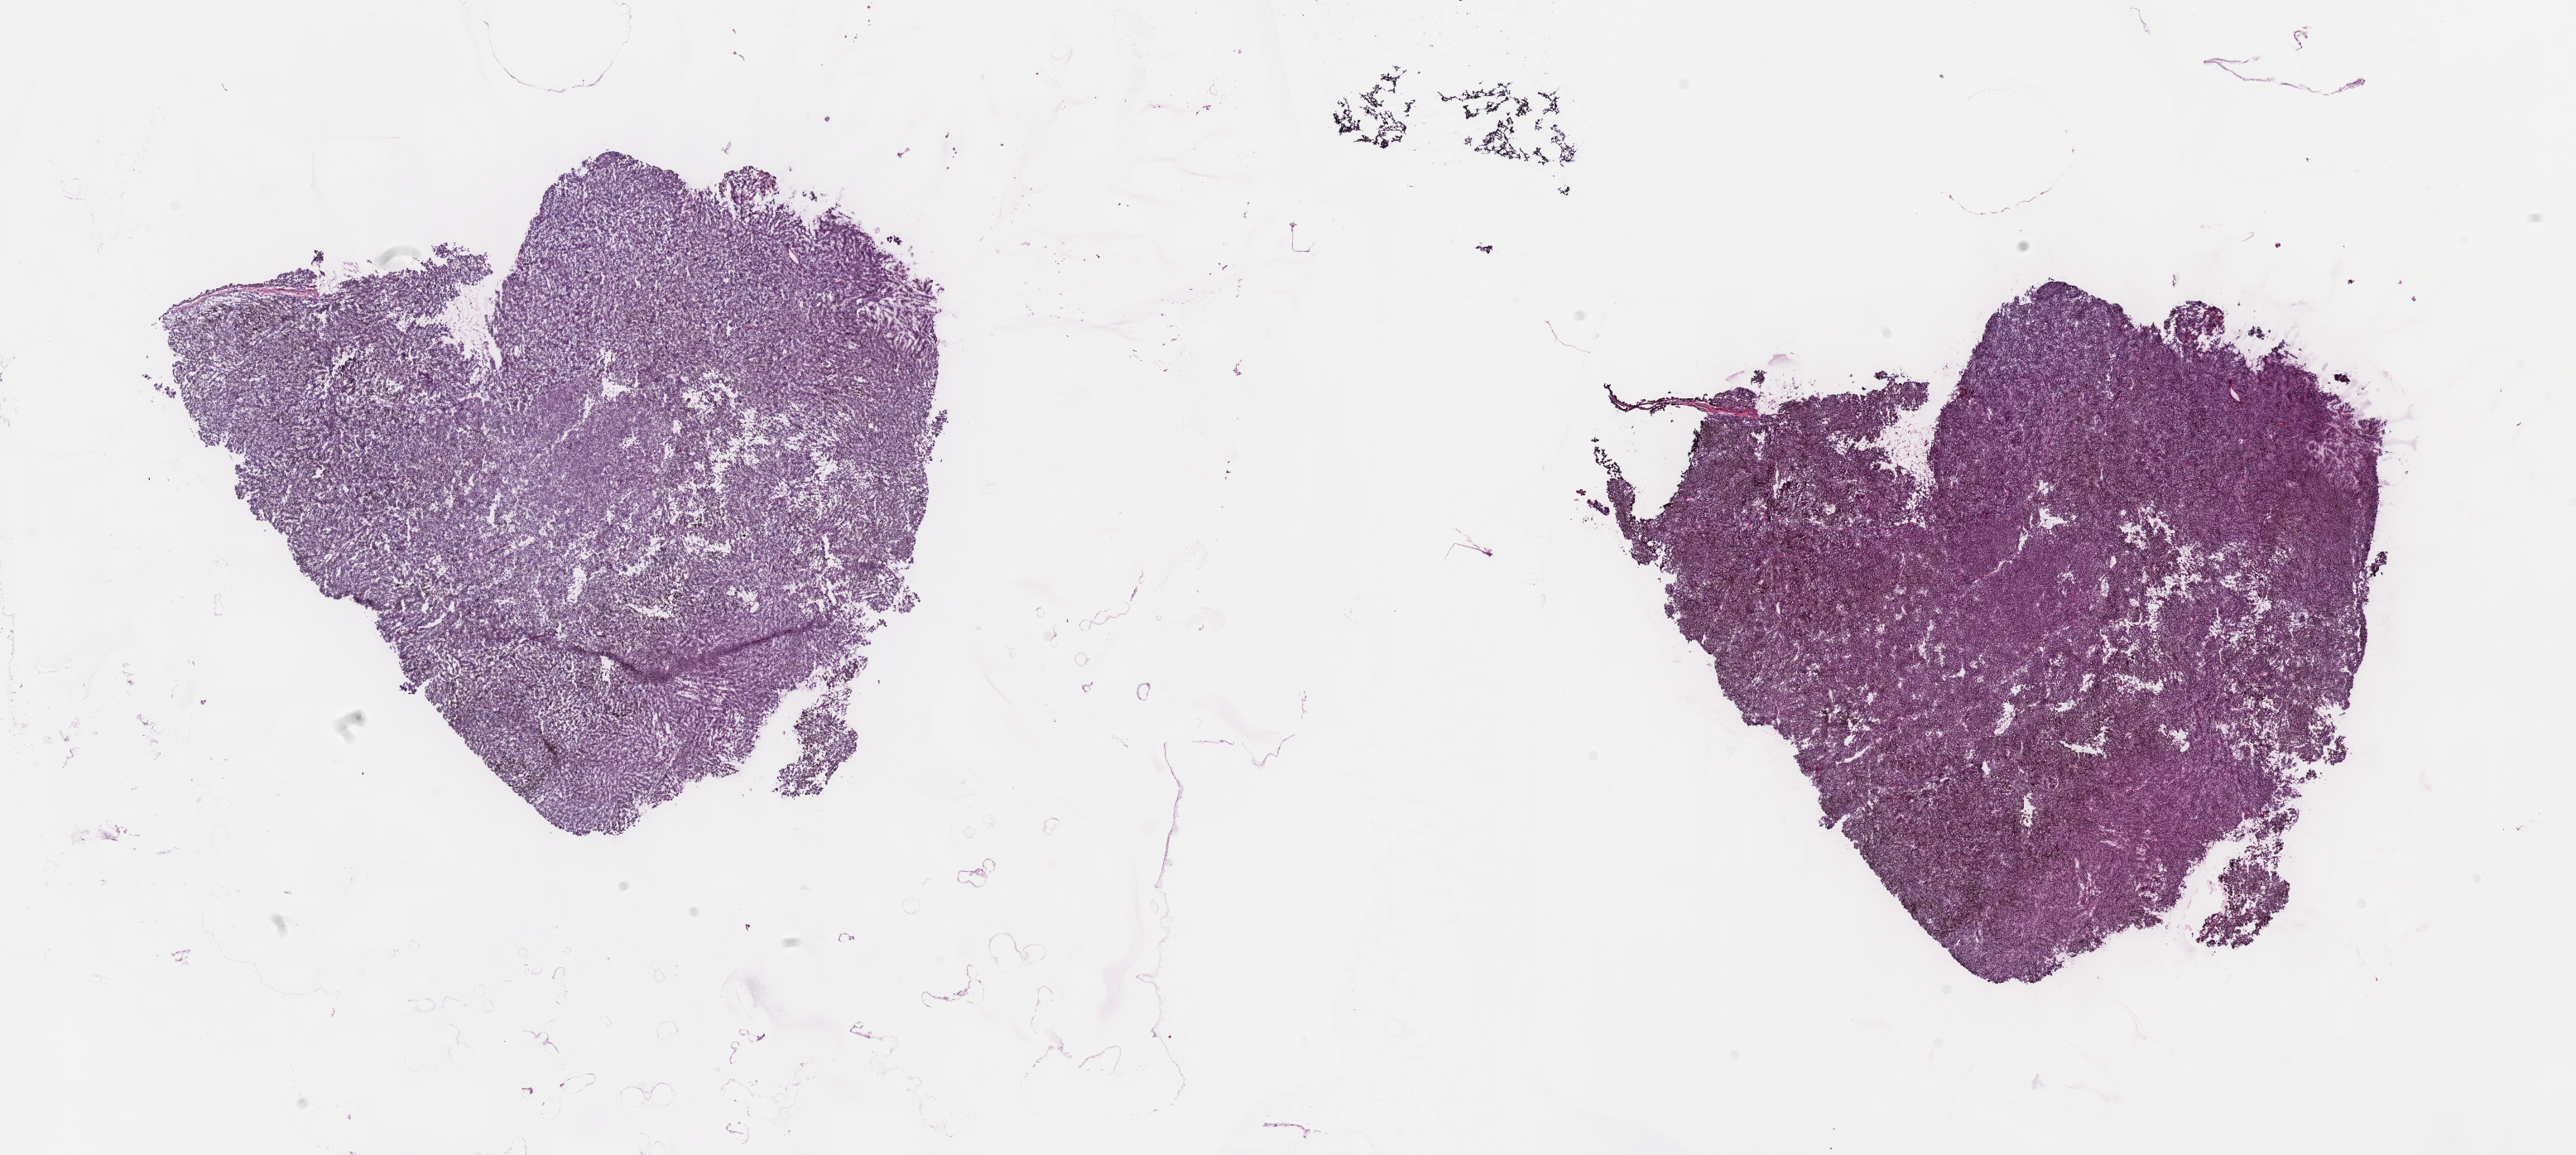
Digitized Hematoxylin and eosin (H&E) stained tissue section (whole slide) — shown as a low-resolution overview of the whole scanned area (about 25.2 x 11.3 mm, from a 40x scan); frozen section; sample: primary tumour, uvea. Male patient; age at initial diagnosis 72 years. Composition of this section per pathologist review: tumour cells 100%, tumour nuclei 80%, normal cells 0%, stromal cells 0%, necrosis 0%. Inflammatory infiltration, as recorded: lymphocyte infiltration 1%, monocyte infiltration 0%, neutrophil infiltration 0%.
• AJCC pathologic stage: IV
• diagnosis: Mixed epithelioid and spindle cell melanoma (choroid)